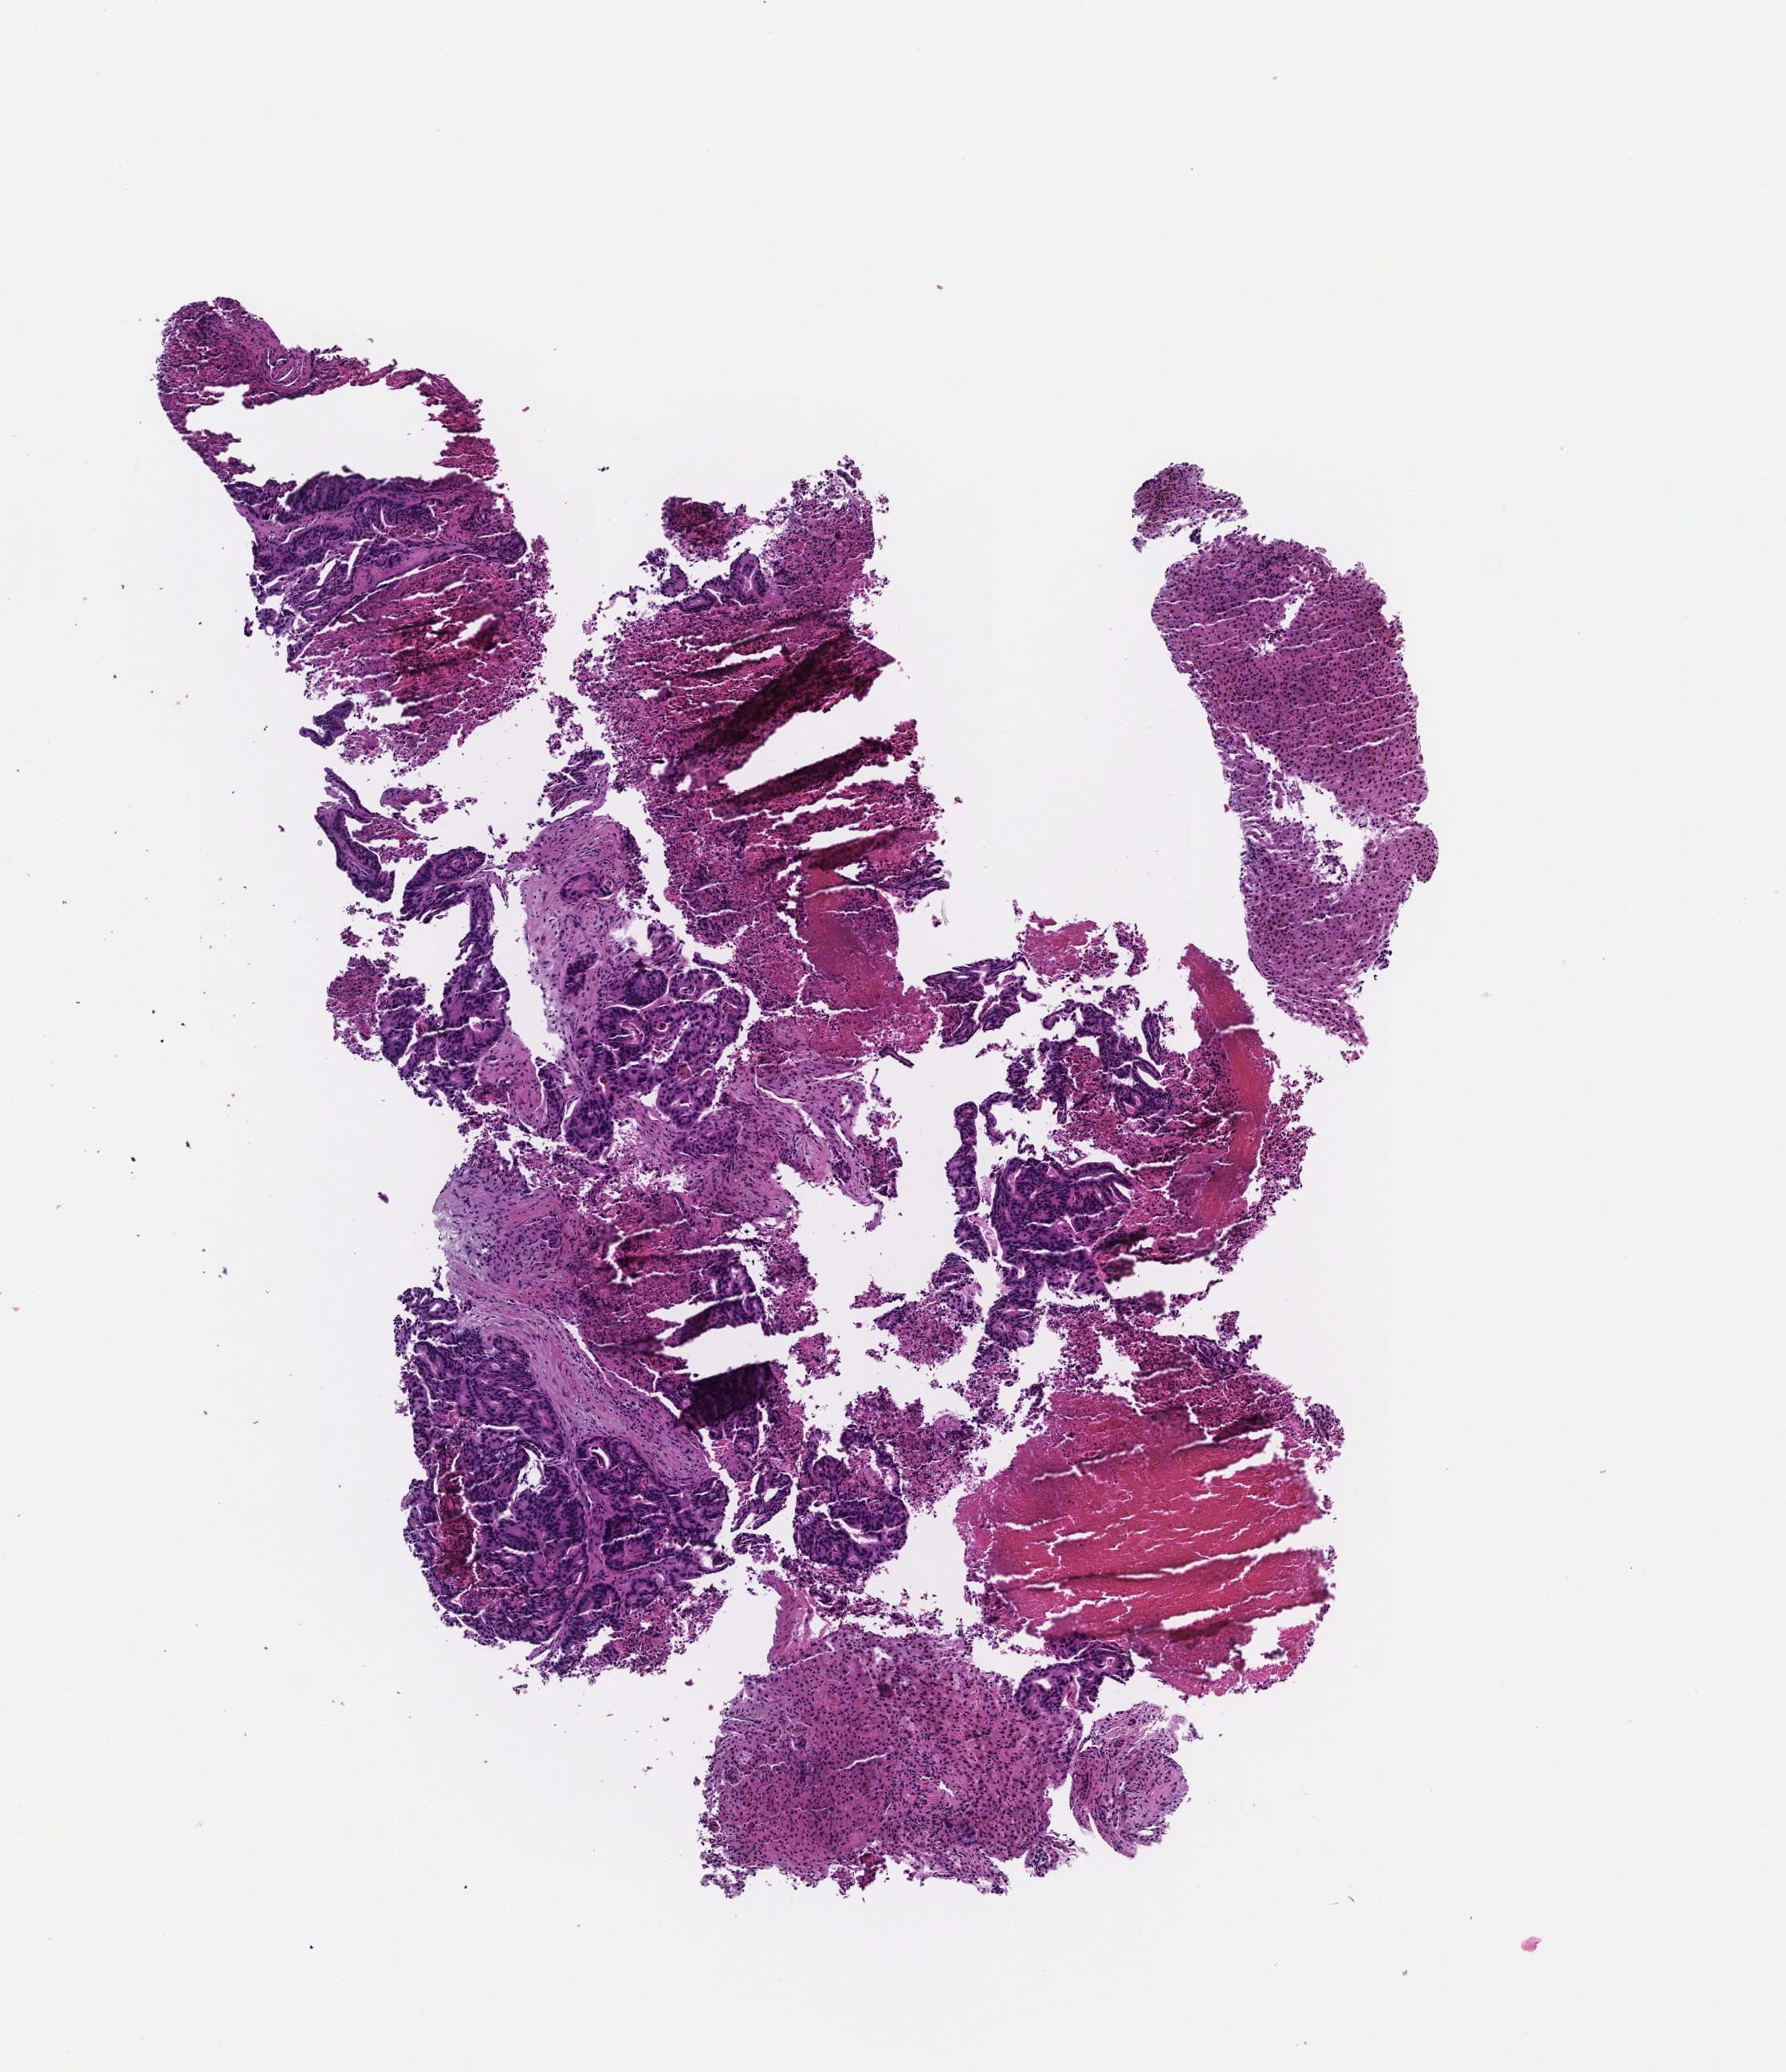
Haematoxylin and eosin whole-slide image — a low-resolution overview of the entire scanned area, about 4.5 x 5.2 mm, formalin-fixed, paraffin-embedded (FFPE) tissue, specimen time point: collected at baseline (before treatment). Female patient.
This section: metastatic tumor tissue. Primary diagnosis of the patient: Colorectal Carcinoma.